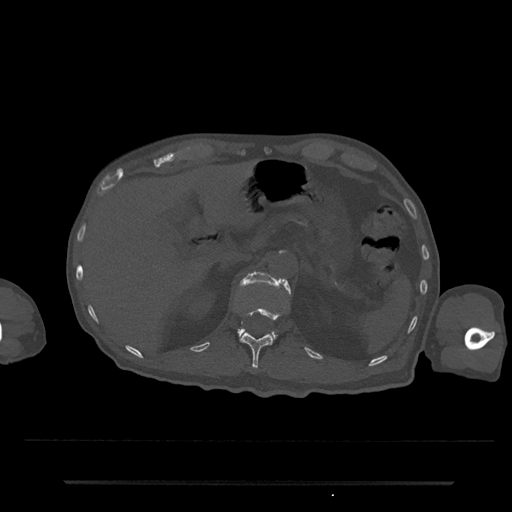
CT including the spine, one axial slice. 120 kVp. Bone window (W 1800 / L 400 HU). 512 × 512 image matrix, field of view 427 × 427 mm. Patient: male, 74 years. From the clinical record (not read from this slice): primary cancer: prostate.
Structures marked on this image (semi-automatic segmentation, software-assisted and operator-edited):
- L1 vertebra: bounding box <237,271,291,338> (left, top, right, bottom; pixels)
- T12 vertebra: <241,307,280,371>